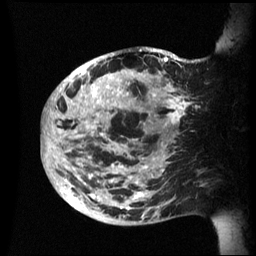
Breast MRI (dynamic contrast-enhanced), one sagittal slice. Position 20 of 60 along the scan axis. Dynamic contrast-enhanced series, image 2 of 3 at this slice position (ordered by acquisition). 1.5 T. TE 4.2 ms, TR 8.4 ms. 256 × 256 image matrix, field of view 230 × 230 mm. Female patient, age 48 years.
Structures marked on this image (semi-automatically segmented with operator editing):
- analysis volume of interest (the breast-tissue region the enhancement analysis was run in; not a lesion): bounding box <42,47,202,226> (left, top, right, bottom; pixels)
- tumour enhancement mask (voxels above the 70 % enhancement threshold inside the analysis volume of interest): <42,49,195,223>